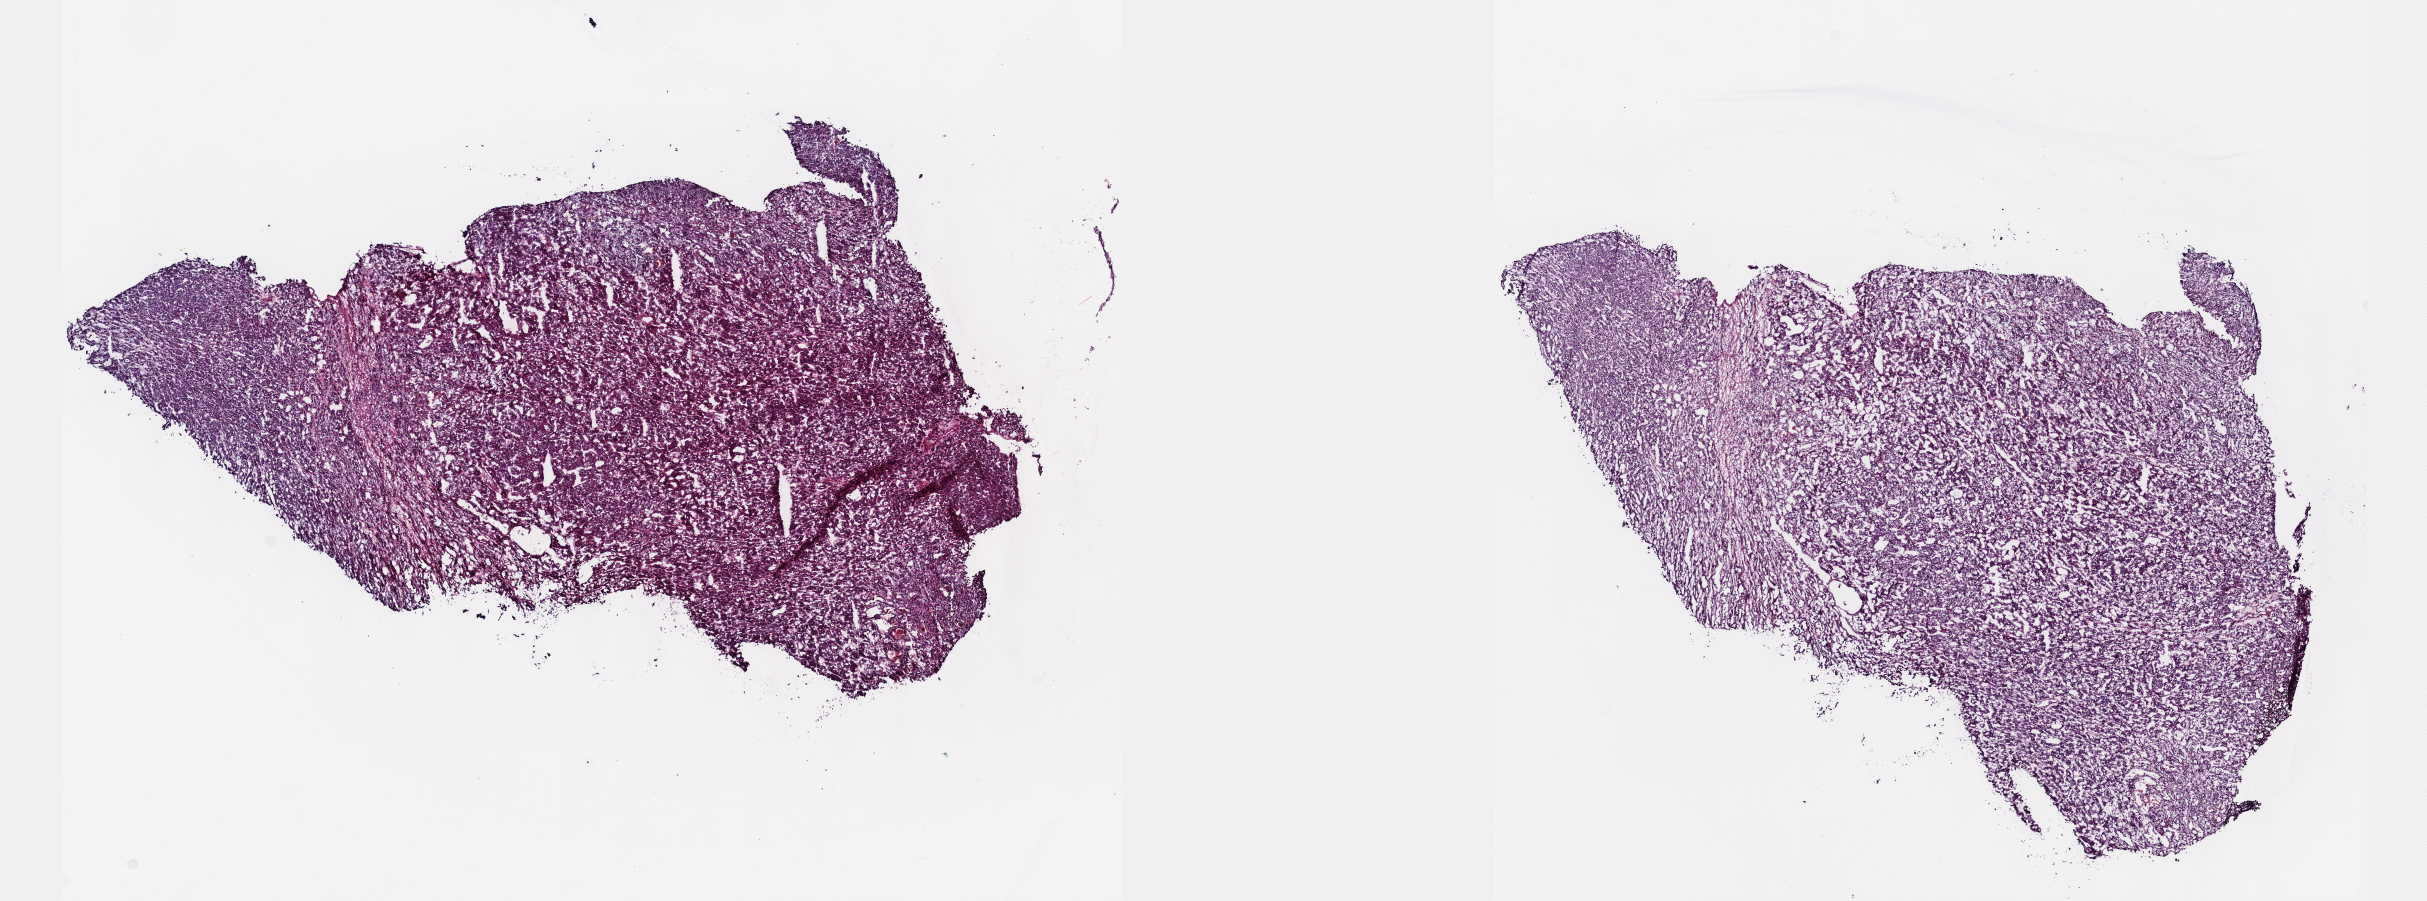
Whole-slide histology image, H&E-stained, shown as a low-resolution overview of the whole scanned area (about 19.6 x 7.3 mm), frozen section, sample: primary tumour, kidney. Patient: male, age at initial diagnosis 63 years. Composition of this section per pathologist review: tumour cells 90%, tumour nuclei 95%, normal cells 0%, stromal cells 10%, necrosis 0%. Infiltration values recorded for this section: lymphocyte infiltration 0%, monocyte infiltration 0%, neutrophil infiltration 0%.
Laterality: left. AJCC pathologic stage: I. Histologic diagnosis: Papillary adenocarcinoma, NOS.